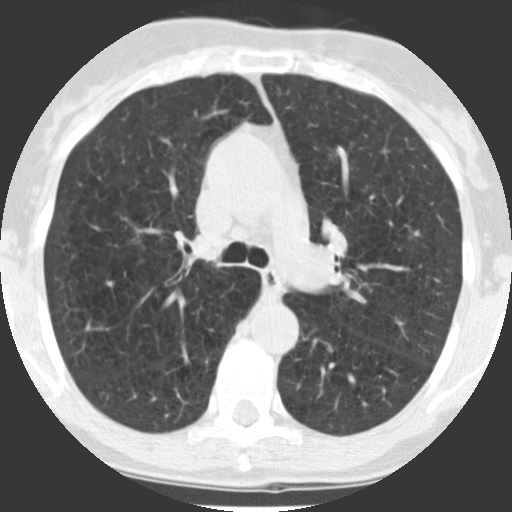
Chest CT (low-dose screening protocol), one axial image. Baseline annual screen. Lung window (W 1500 / L -600 HU). 2.5 mm slice thickness. 120 kVp. 512 × 512 image matrix, field of view 280 × 280 mm. Female, age 71 years at enrolment. Current smoker at enrolment.
Expert reader's lesion annotation, bounding box [x1, y1, x2, y2] px = [317, 329, 350, 362]. Screening reader's record for this exam: no non-calcified nodule ≥4 mm recorded. Later outcome: lung cancer diagnosed 802 days after this screen (after the third annual screen) — squamous cell carcinoma, NOS, left lower lobe, poorly differentiated (G3), stage IB (AJCC 6th edition), 40 mm at pathology.